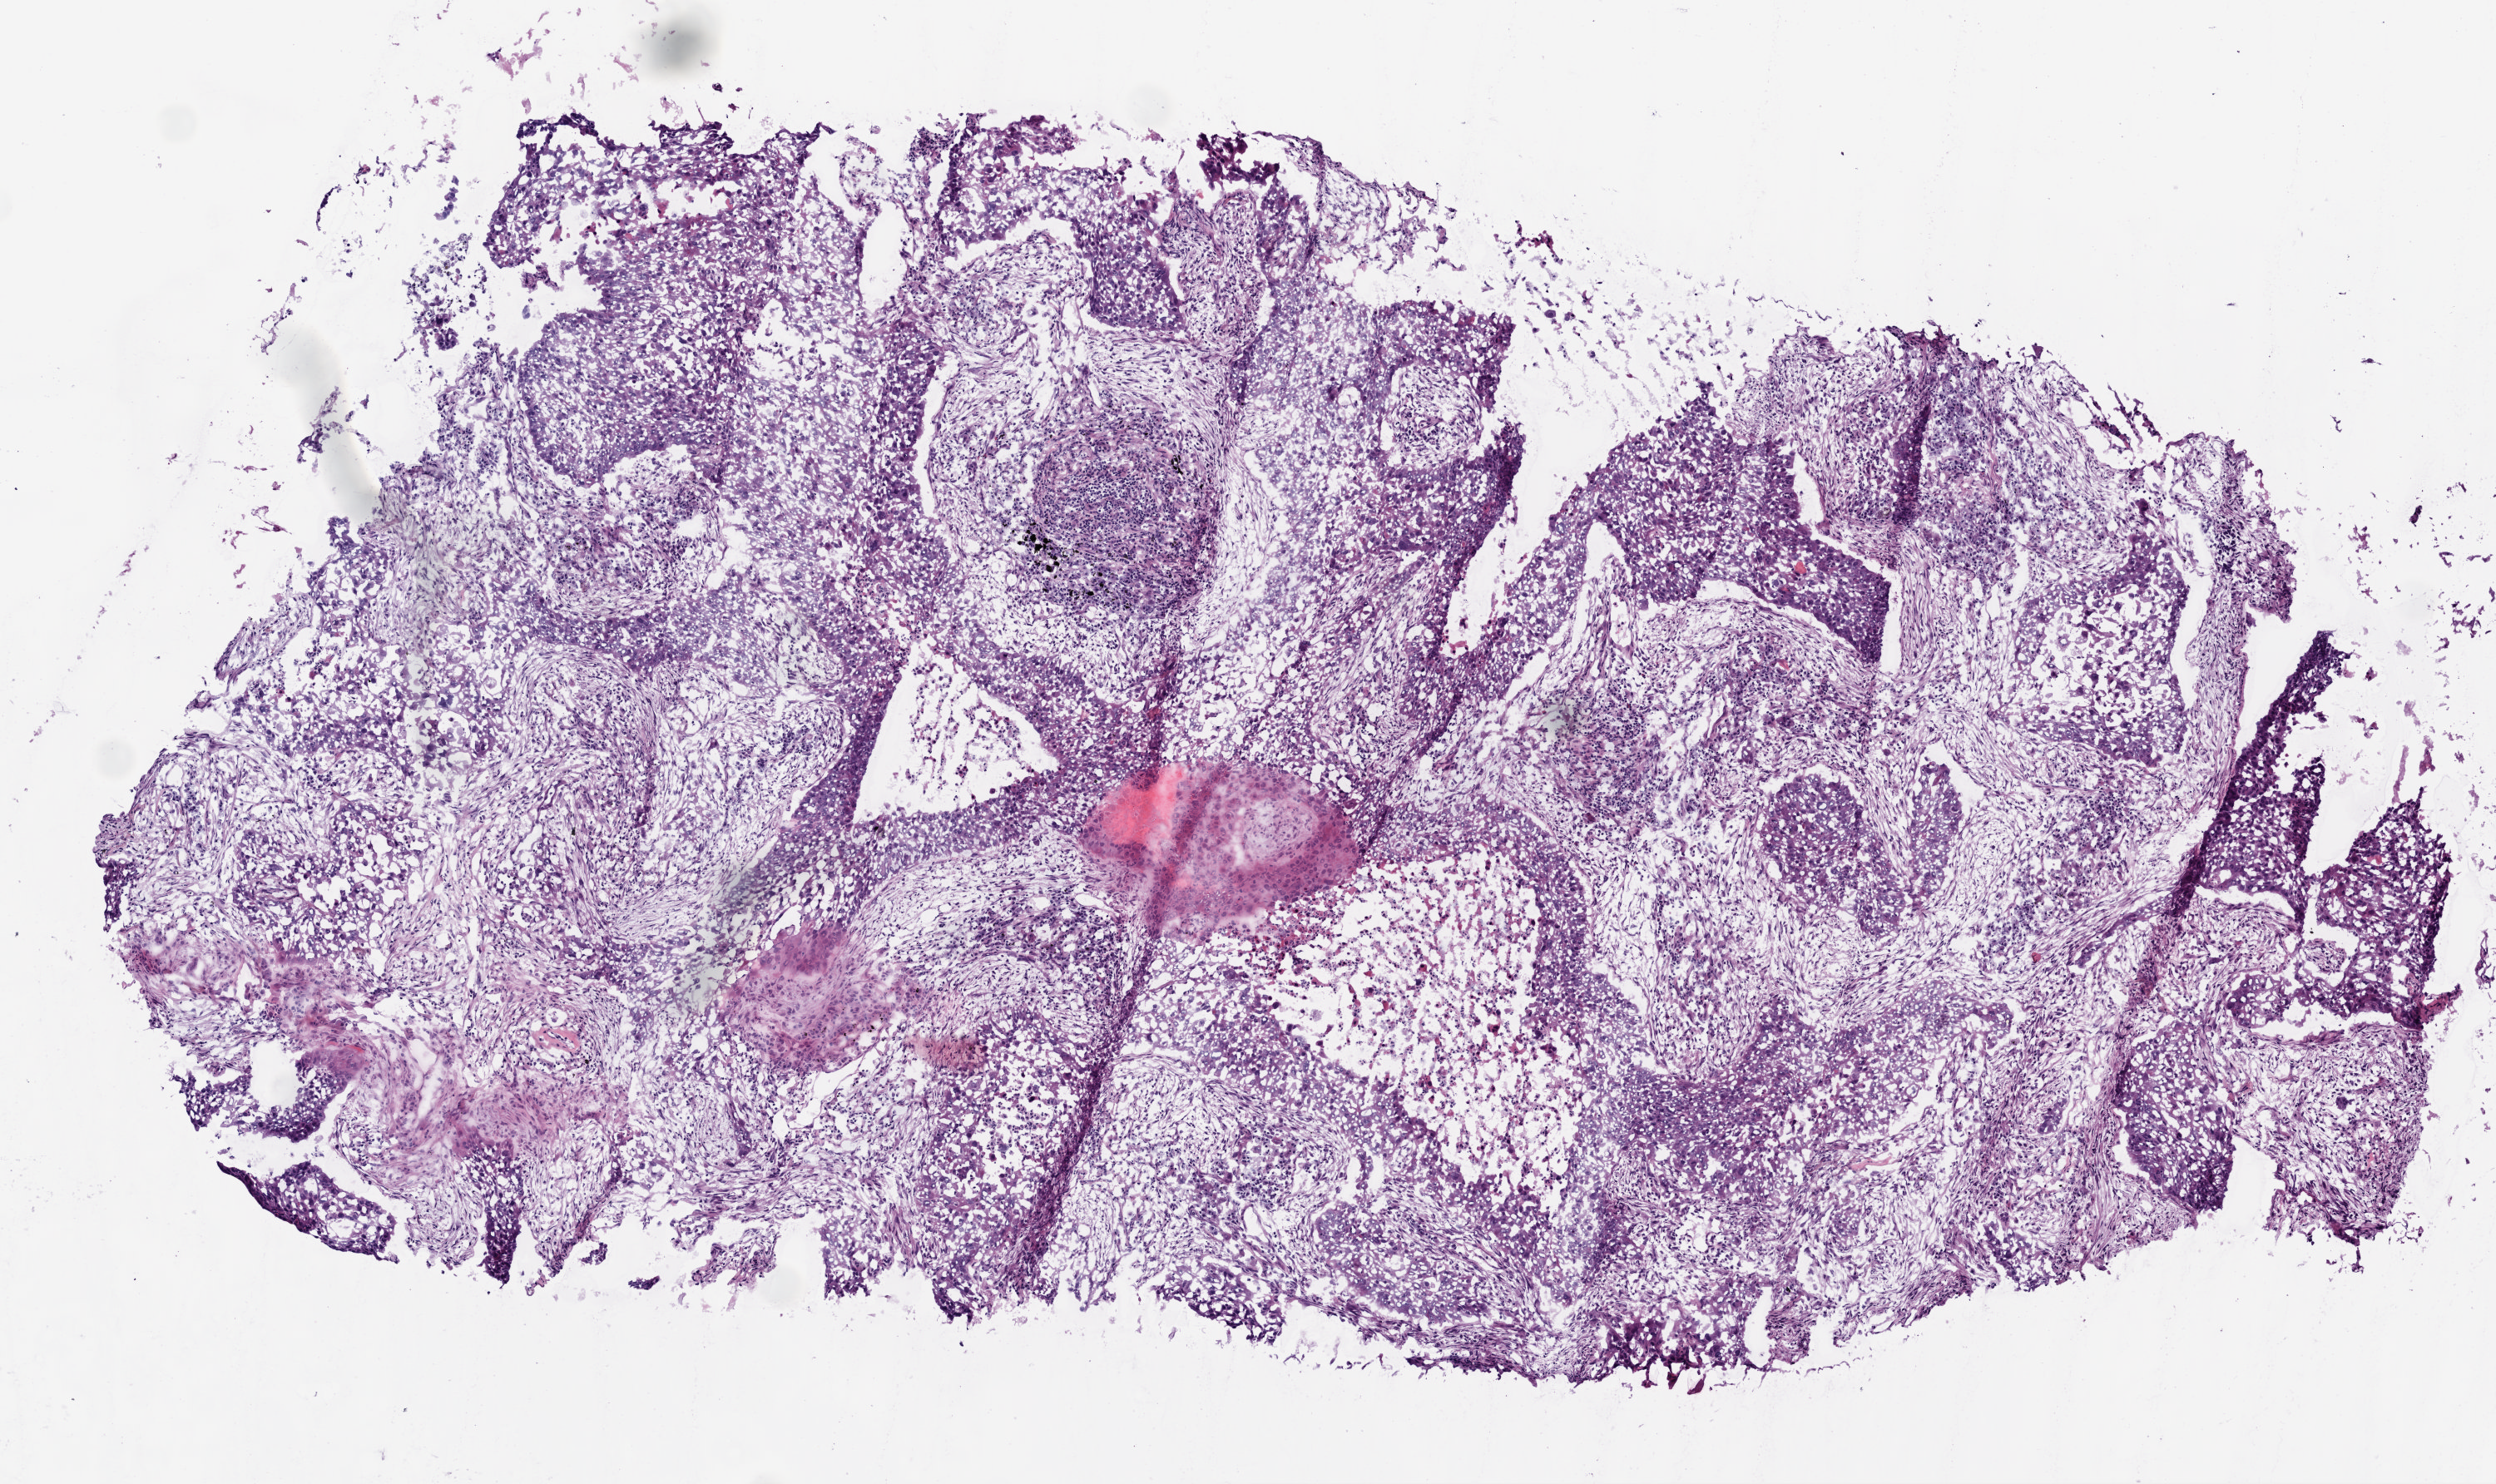
Digitized H&E tissue section (whole slide) — a low-resolution overview of the entire scanned area, about 6.0 x 3.6 mm (slide scanned at 20x), frozen section from the bottom of the tissue portion, primary tumour sample from the lung. Male, age 65 years at initial diagnosis. Composition of this section per pathologist review: tumour cells 50%, tumour nuclei 70%, normal cells 0%, stromal cells 40%, necrosis 10%. Inflammatory infiltration, as recorded: lymphocyte infiltration 2%.
- pathologic diagnosis: Squamous cell carcinoma, NOS
- TNM: T2 N1 M1
- AJCC pathologic stage: IV